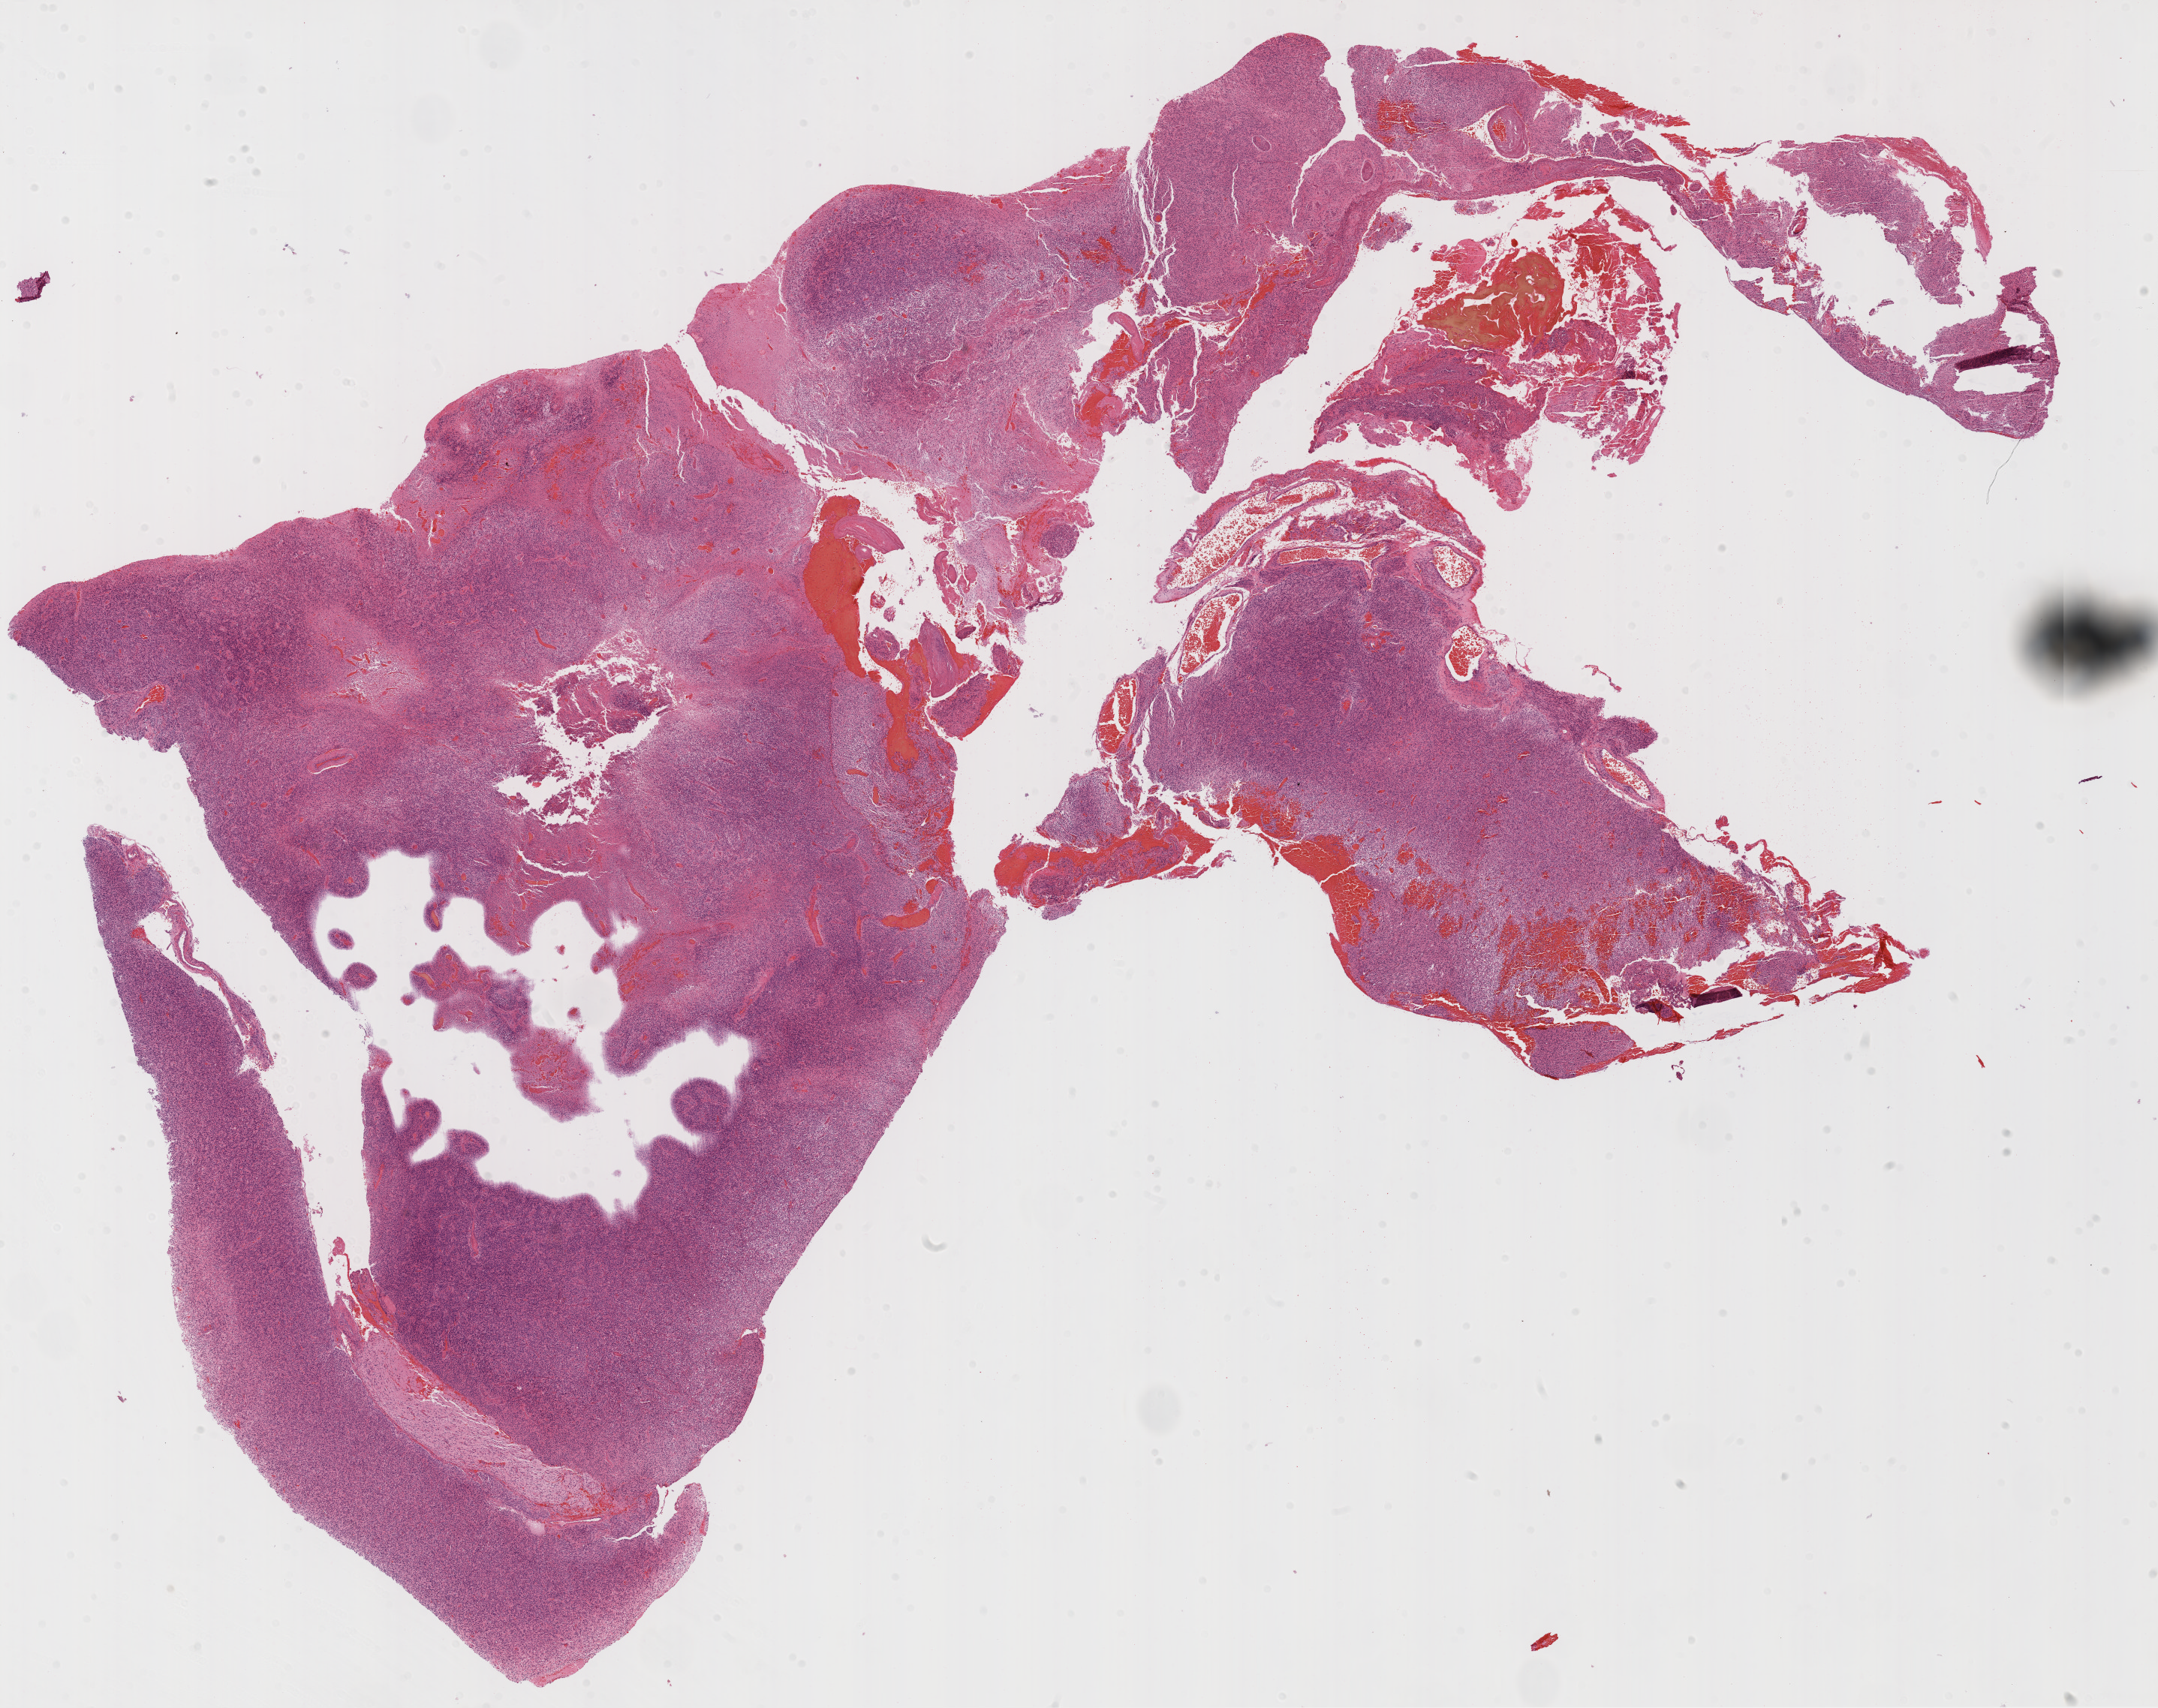
H&E-stained whole-slide image — shown as a low-resolution overview of the whole scanned area (about 23.1 x 18.3 mm, acquisition: 20x scan); FFPE section; brain, primary tumour sample. Patient: male, age at initial diagnosis 76 years.
Pathologic diagnosis: Glioblastoma.